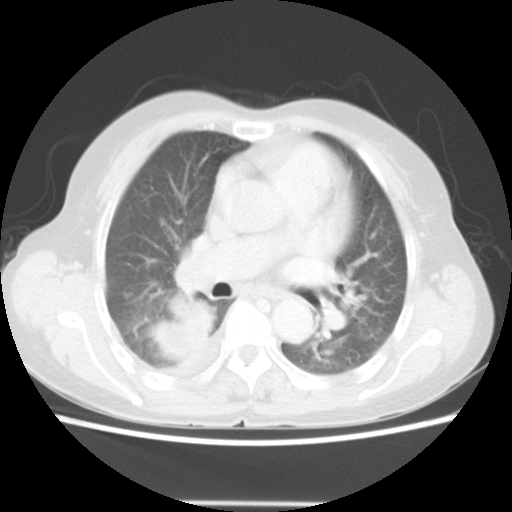
Chest CT, one axial slice; position 29 of 52 along the scan axis; reconstruction kernel STANDARD; lung window (W 1500 / L -600 HU); 5 mm slice thickness; 512 × 512 image matrix, field of view 337 × 337 mm. Patient: female, 67 years. From the clinical record (not read from this slice): clinical TNM (as recorded): T3 N1 M1.
Structures marked on this image (bounding box drawn by a radiologist):
- lung tumour (recorded histology: adenocarcinoma): bounding box <146,292,218,360> (left, top, right, bottom; pixels)